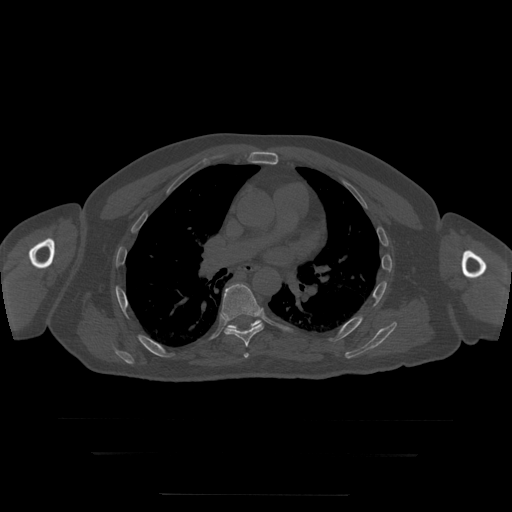
CT including the spine, one axial slice; bone window (W 1800 / L 400 HU); 512 × 512 image matrix, field of view 510 × 510 mm. Patient age 73 years. From the clinical record (not read from this slice): primary cancer: prostate.
Annotated regions visible in this slice (semi-automatic segmentation, software-assisted and operator-edited):
- T6 vertebra: bounding box <244,354,249,358> (left, top, right, bottom; pixels)
- T7 vertebra: <222,284,264,347>
- T8 vertebra: <227,320,261,331>